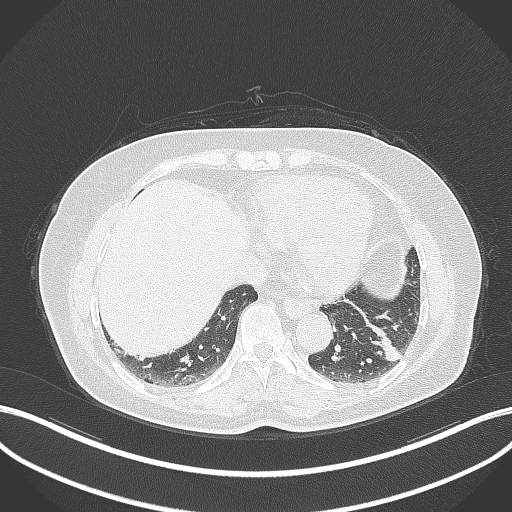
Chest CT, one axial slice. Slice 112 of 311 in the series (ordered by position). Lung window (W 1500 / L -600 HU). 512 × 512 image matrix, field of view 400 × 400 mm. Patient: female, 59 years. From the clinical record (not read from this slice): clinical TNM (as recorded): T2a N0 M0; histopathological grade: G2-3.
Outlined on this slice (bounding box drawn by a radiologist):
- lung tumour (recorded histology: adenocarcinoma): bounding box [x1, y1, x2, y2] px = [373, 326, 405, 364]